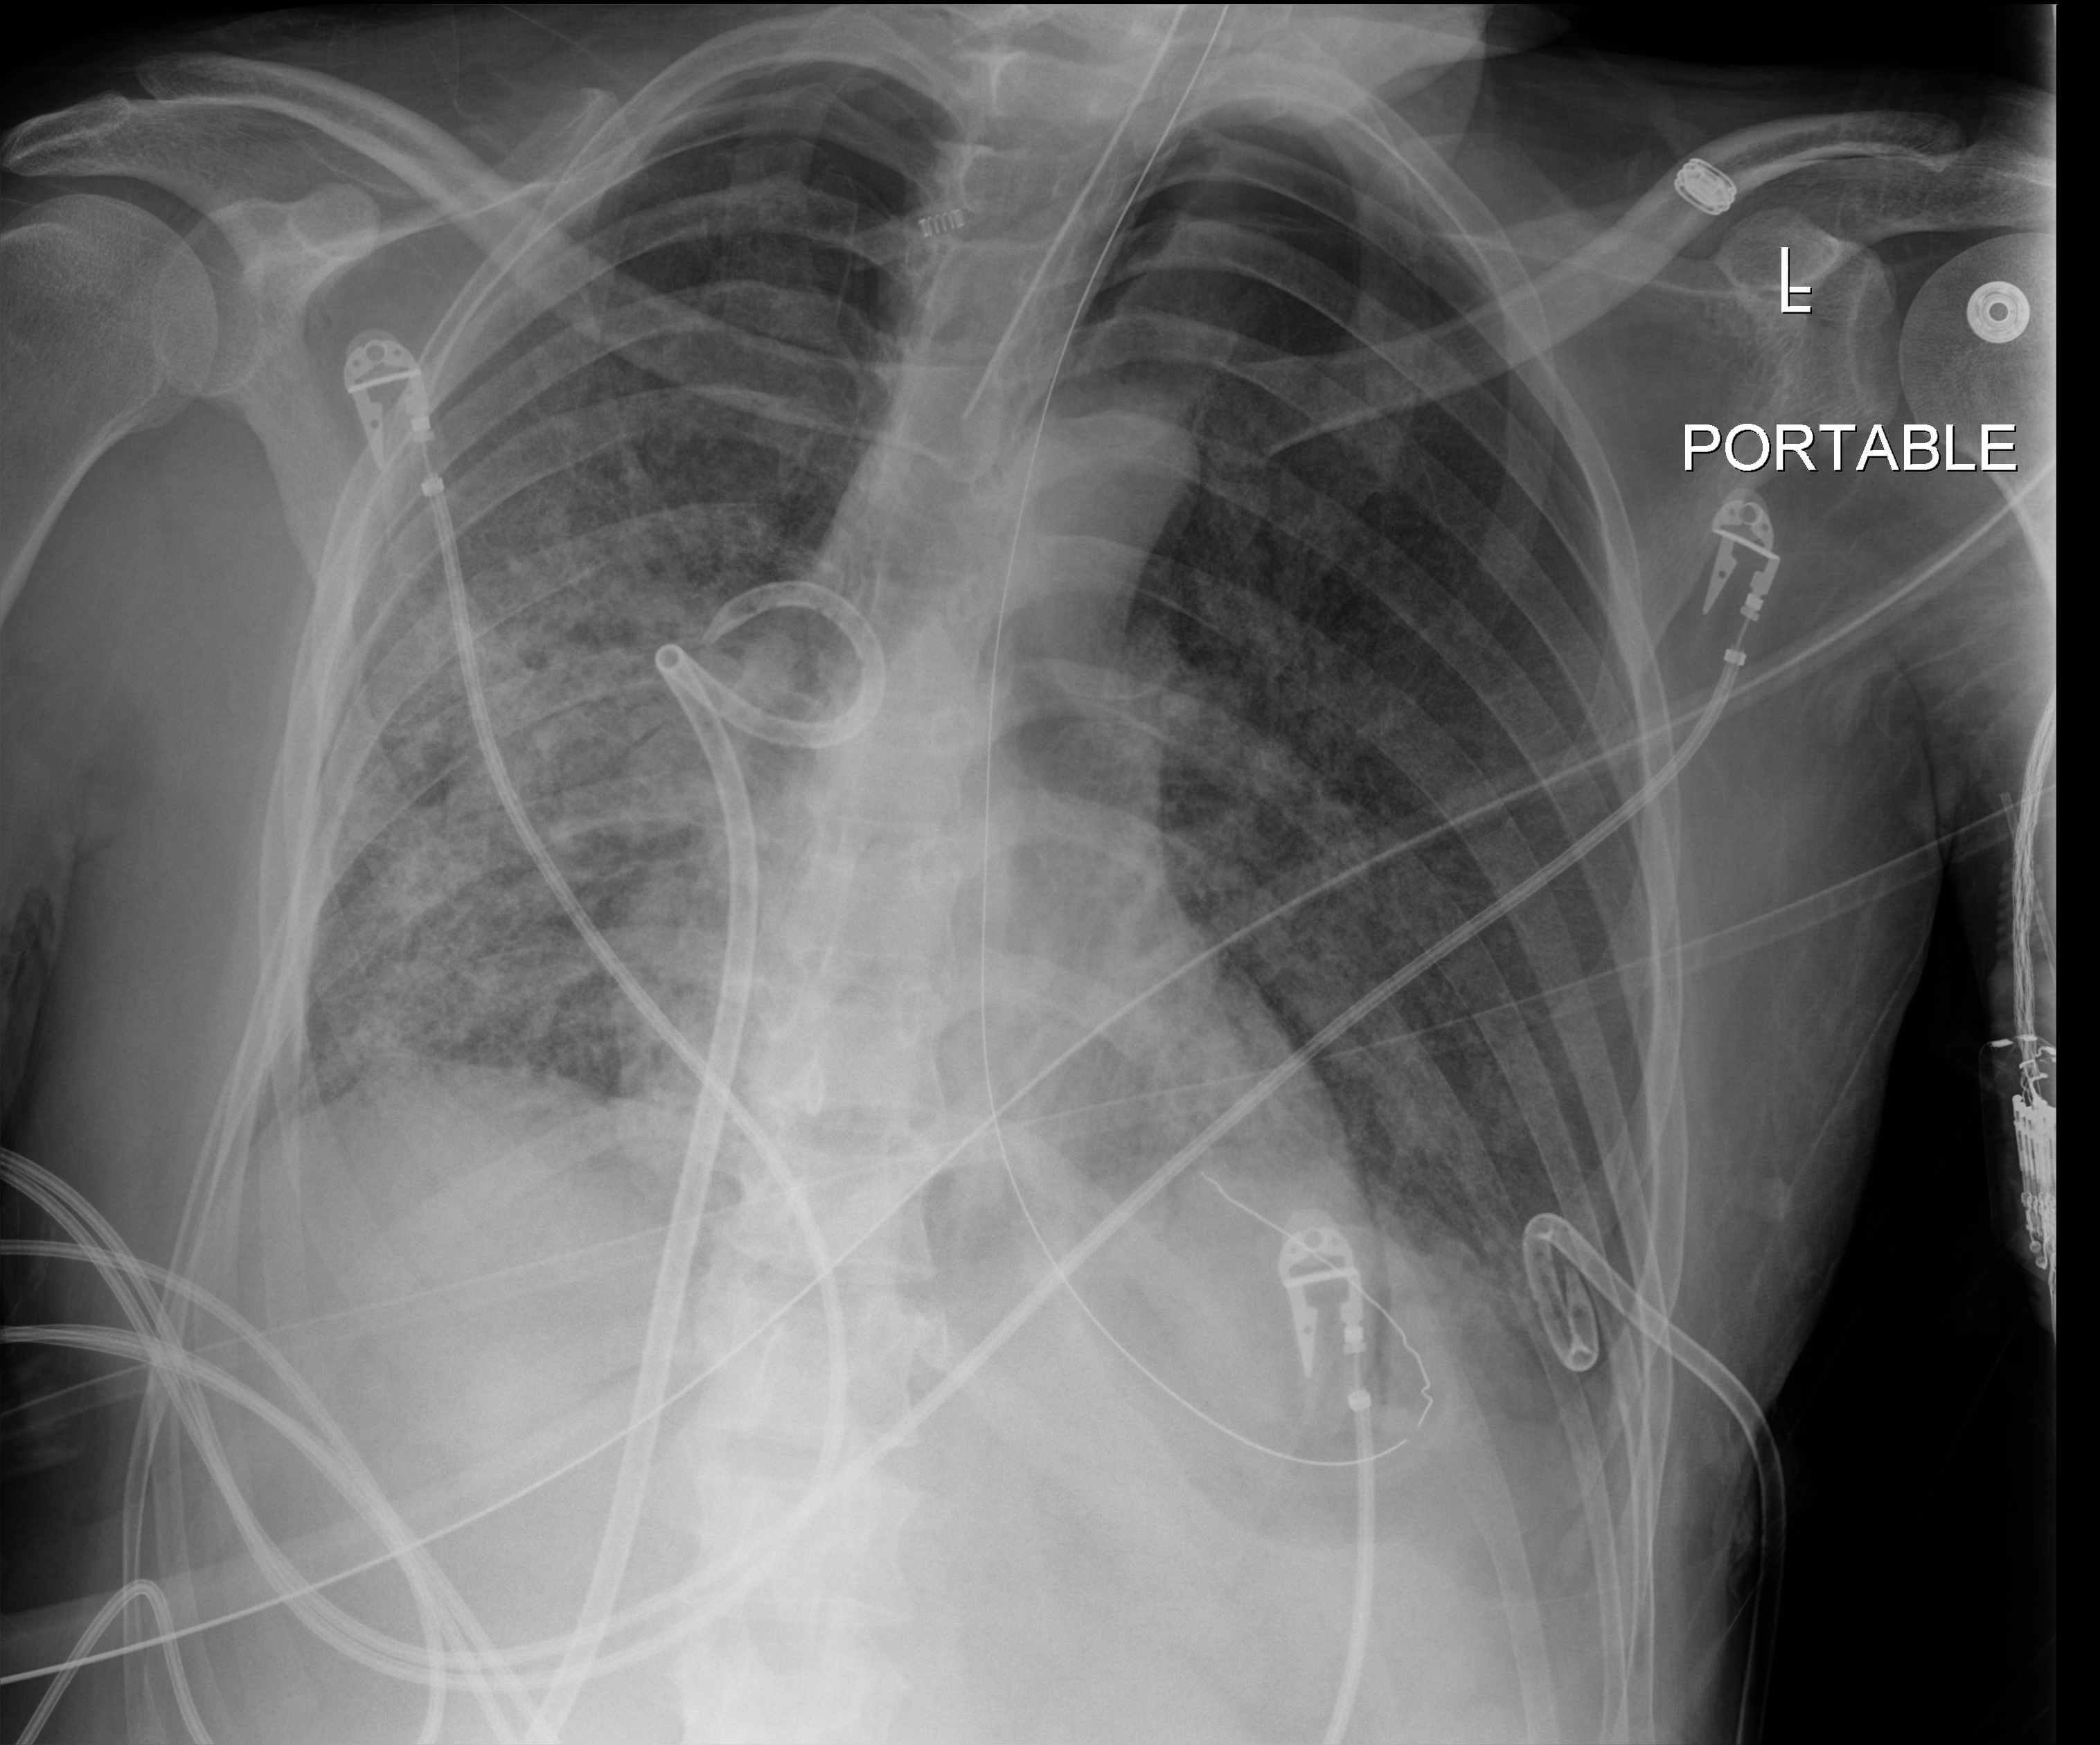
Bedside chest radiograph (digital radiography). Patient hospitalised with COVID-19, aged 18–59 years.
From the hospital-stay record, not from the radiograph (when in the stay this image was taken is not recorded): mechanically ventilated during this hospital stay: yes; other chronic lung disease (admission record): no; hypertension (admission record): no.